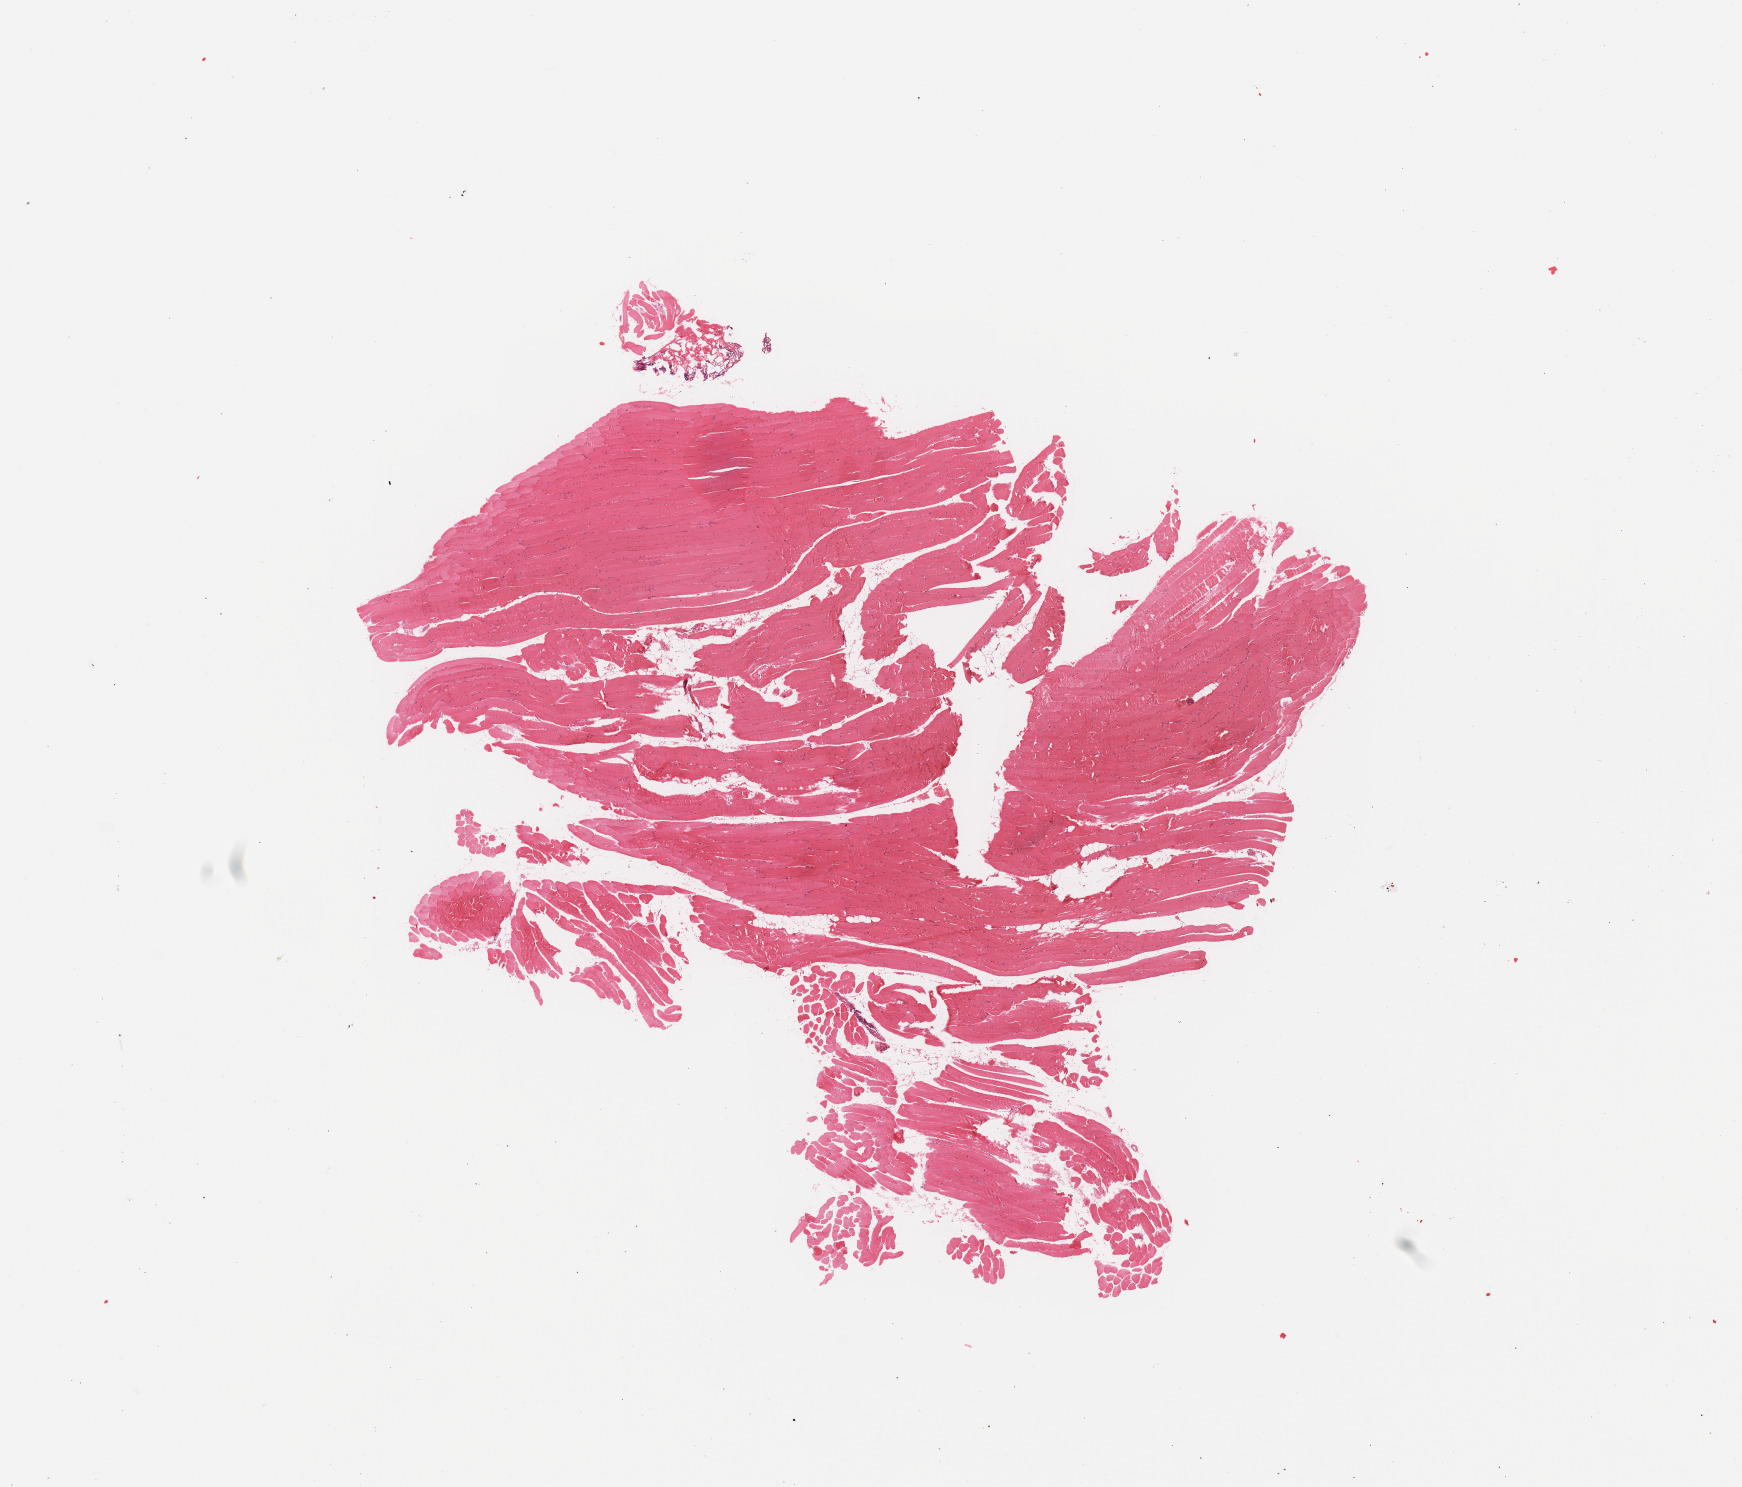
Whole-slide histology image, Hematoxylin and eosin (H&E) stained — low-resolution overview of the scanned area, about 13.8 x 11.8 mm (from a 20x scan). 50-year-old male patient.
* patient diagnosis (cohort enrolment): sarcoma (site not recorded at cohort level)
* primary tumour site (as recorded): pelvic